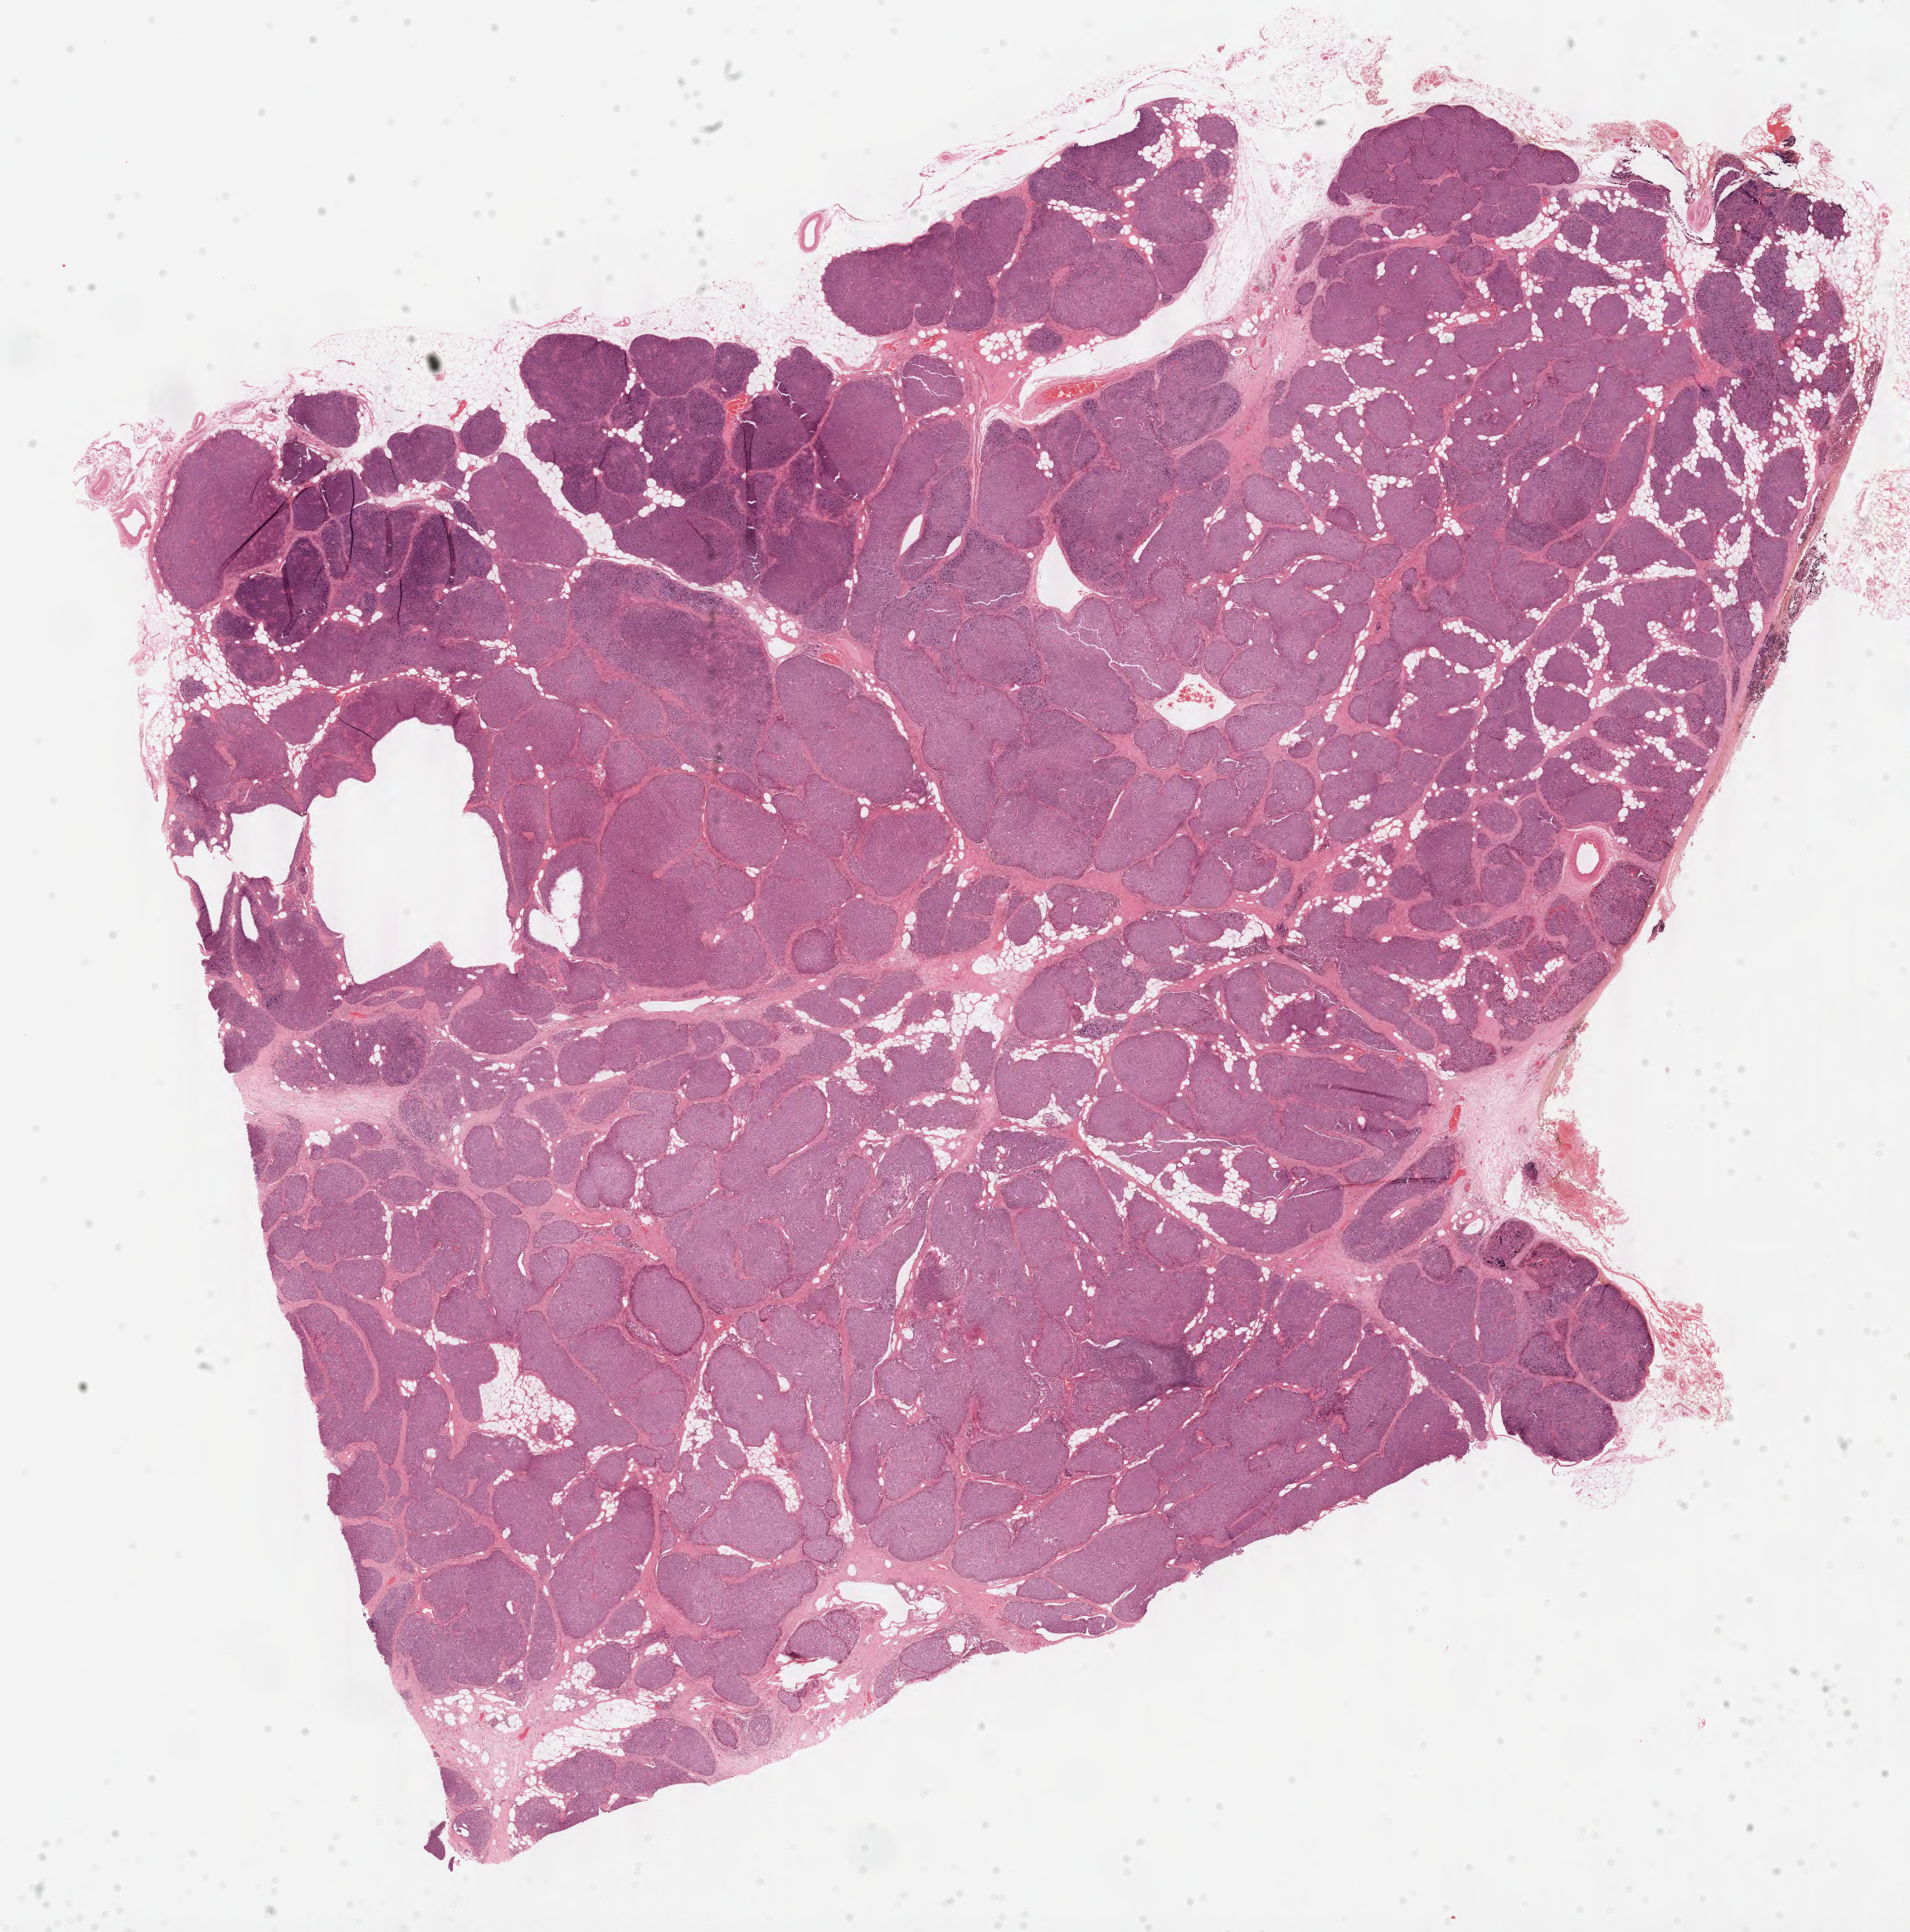
Digitized H&E tissue section (whole slide), low-resolution overview of the scanned area, about 18.2 x 18.4 mm (acquisition: 40x scan), formalin-fixed paraffin-embedded (FFPE) diagnostic section, primary tumour sample from the thymus. Male, age 43 years at initial diagnosis.
- histologic diagnosis: Thymoma, type B3, malignant